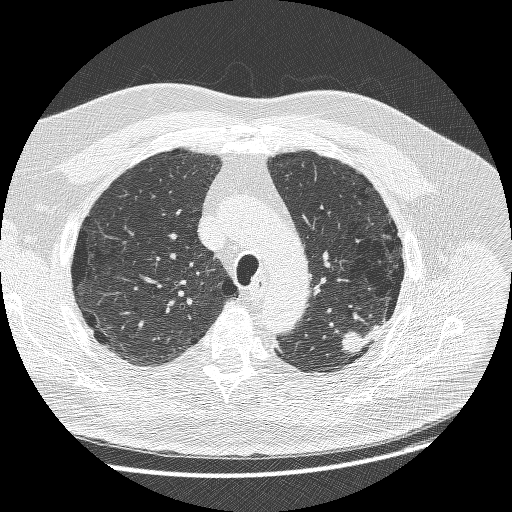
Axial slice from a low-dose chest CT screening exam. Baseline annual screen. Lung window (W 1500 / L -600 HU). Lung (sharp) reconstruction kernel (BONE). Slice 199 of 258 in the series. Male participant, aged 68 years at enrolment. Former smoker at enrolment.
Expert reader's lesion annotation, bounding box [x1, y1, x2, y2] px = [333, 314, 389, 363]. Reader record for this screening exam (exam-level; its link to the box is not recorded): non-calcified nodule or mass ≥4 mm, left upper lobe, 15 × 14 mm, smooth margins, soft tissue attenuation. Participant outcome: lung cancer diagnosed 19 days after this screen — adenosquamous carcinoma, left upper lobe, poorly differentiated (G3), stage IIIB (AJCC 6th edition), 32 mm at pathology.